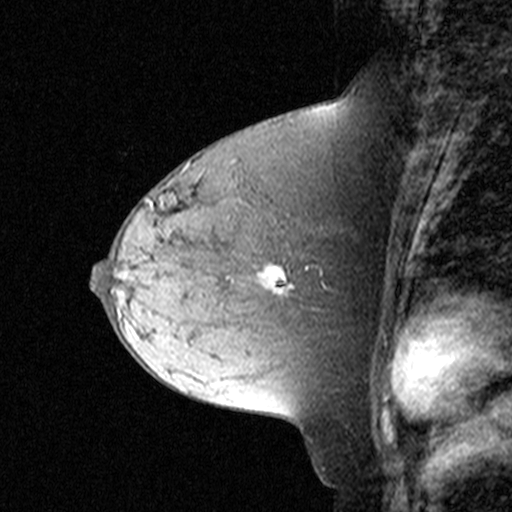
Breast MRI (dynamic contrast-enhanced), one sagittal slice. Slice 18 of 44 in the series (ordered by position). Dynamic contrast-enhanced study with each time point stored as its own series, time point 2 of 3 at this slice position (early post-contrast, ordered by acquisition time). 1.5 T. TE 4.5 ms, TR 11 ms. 3 mm slice thickness. 512 × 512 image matrix. Female patient, age 44 years. From the clinical record (not read from this slice): setting: breast cancer imaged before/during neoadjuvant chemotherapy; receptor status: triple-negative.
Structures marked on this image (semi-automatically segmented with operator editing):
- analysis volume of interest (the breast-tissue region the enhancement analysis was run in; not a lesion): bounding box <174,204,303,305> (left, top, right, bottom; pixels)
- tumour enhancement mask (voxels above the 90 % enhancement threshold inside the analysis volume of interest): <259,265,292,294>